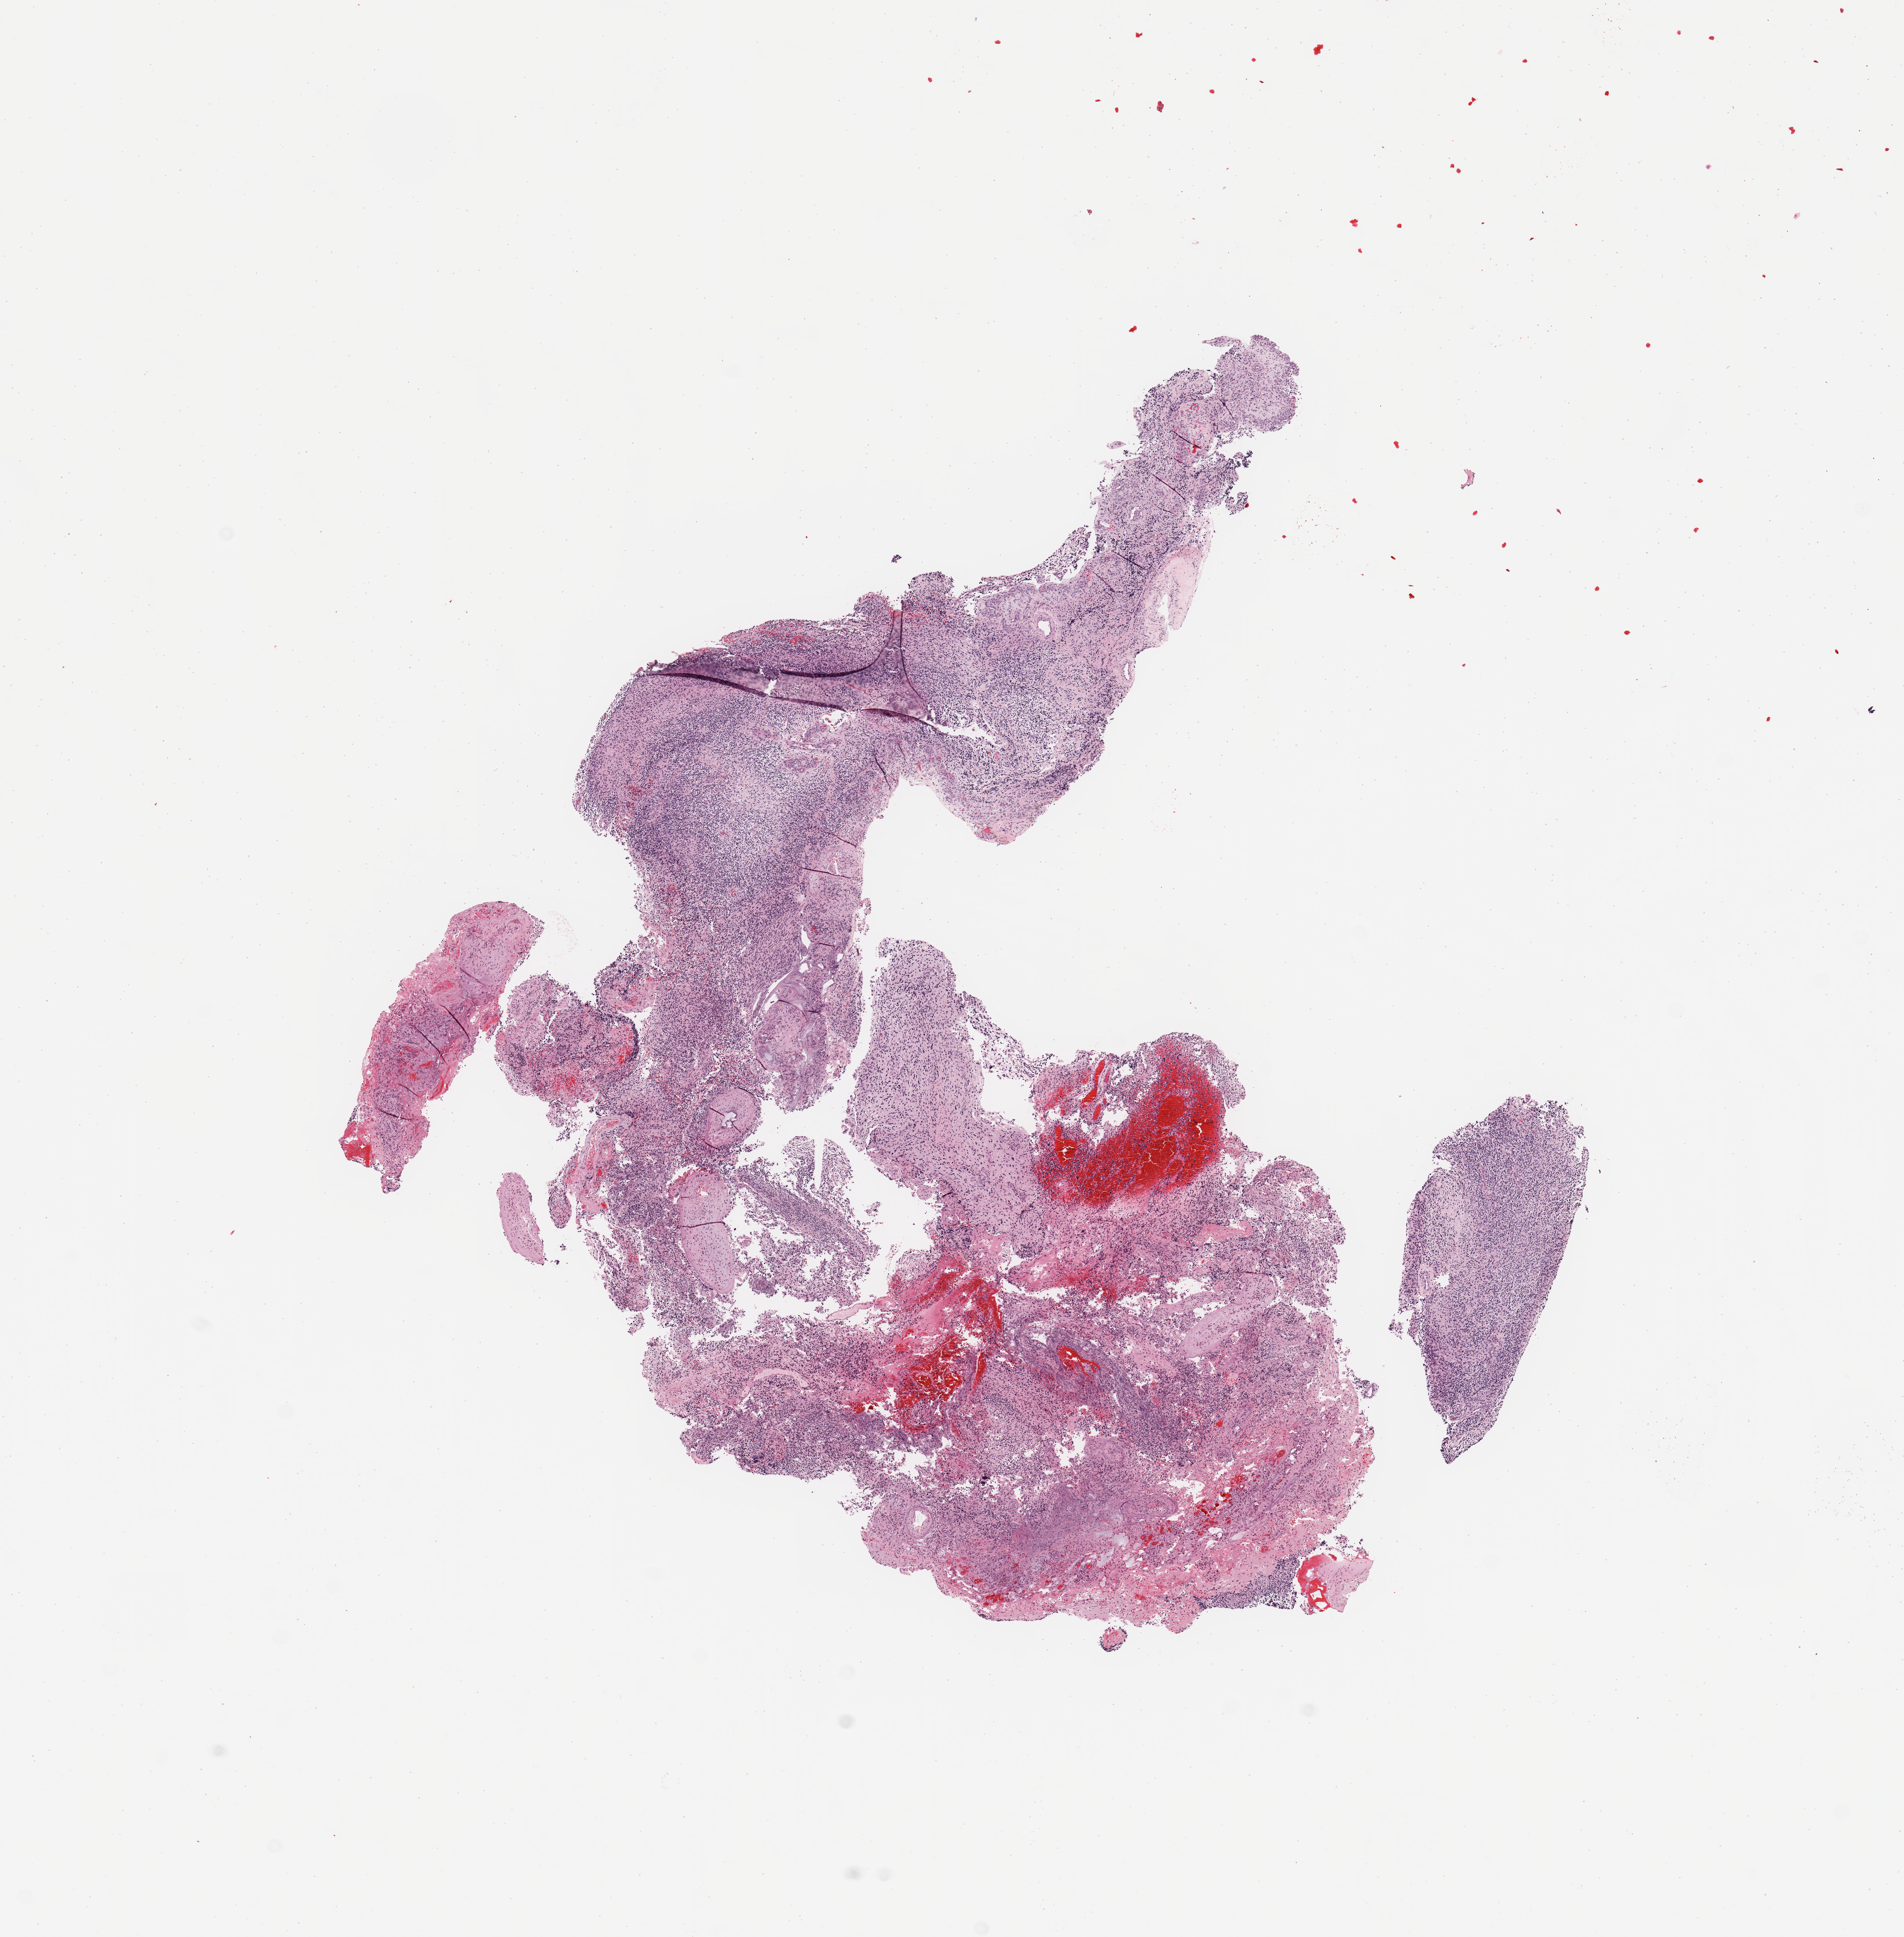
Whole-slide histology image, H&E, whole scanned area (about 11.8 x 12.0 mm, slide scanned at 20x) shown as a low-resolution overview, tumour tissue sample, sampled site: brain. Patient: female, age 58 years. Pathologist review of this section (percent, as recorded): tumour nuclei 75%, necrosis 5%.
Primary tumour site (as recorded): temporal lobe. Histologic diagnosis: Glioblastoma.